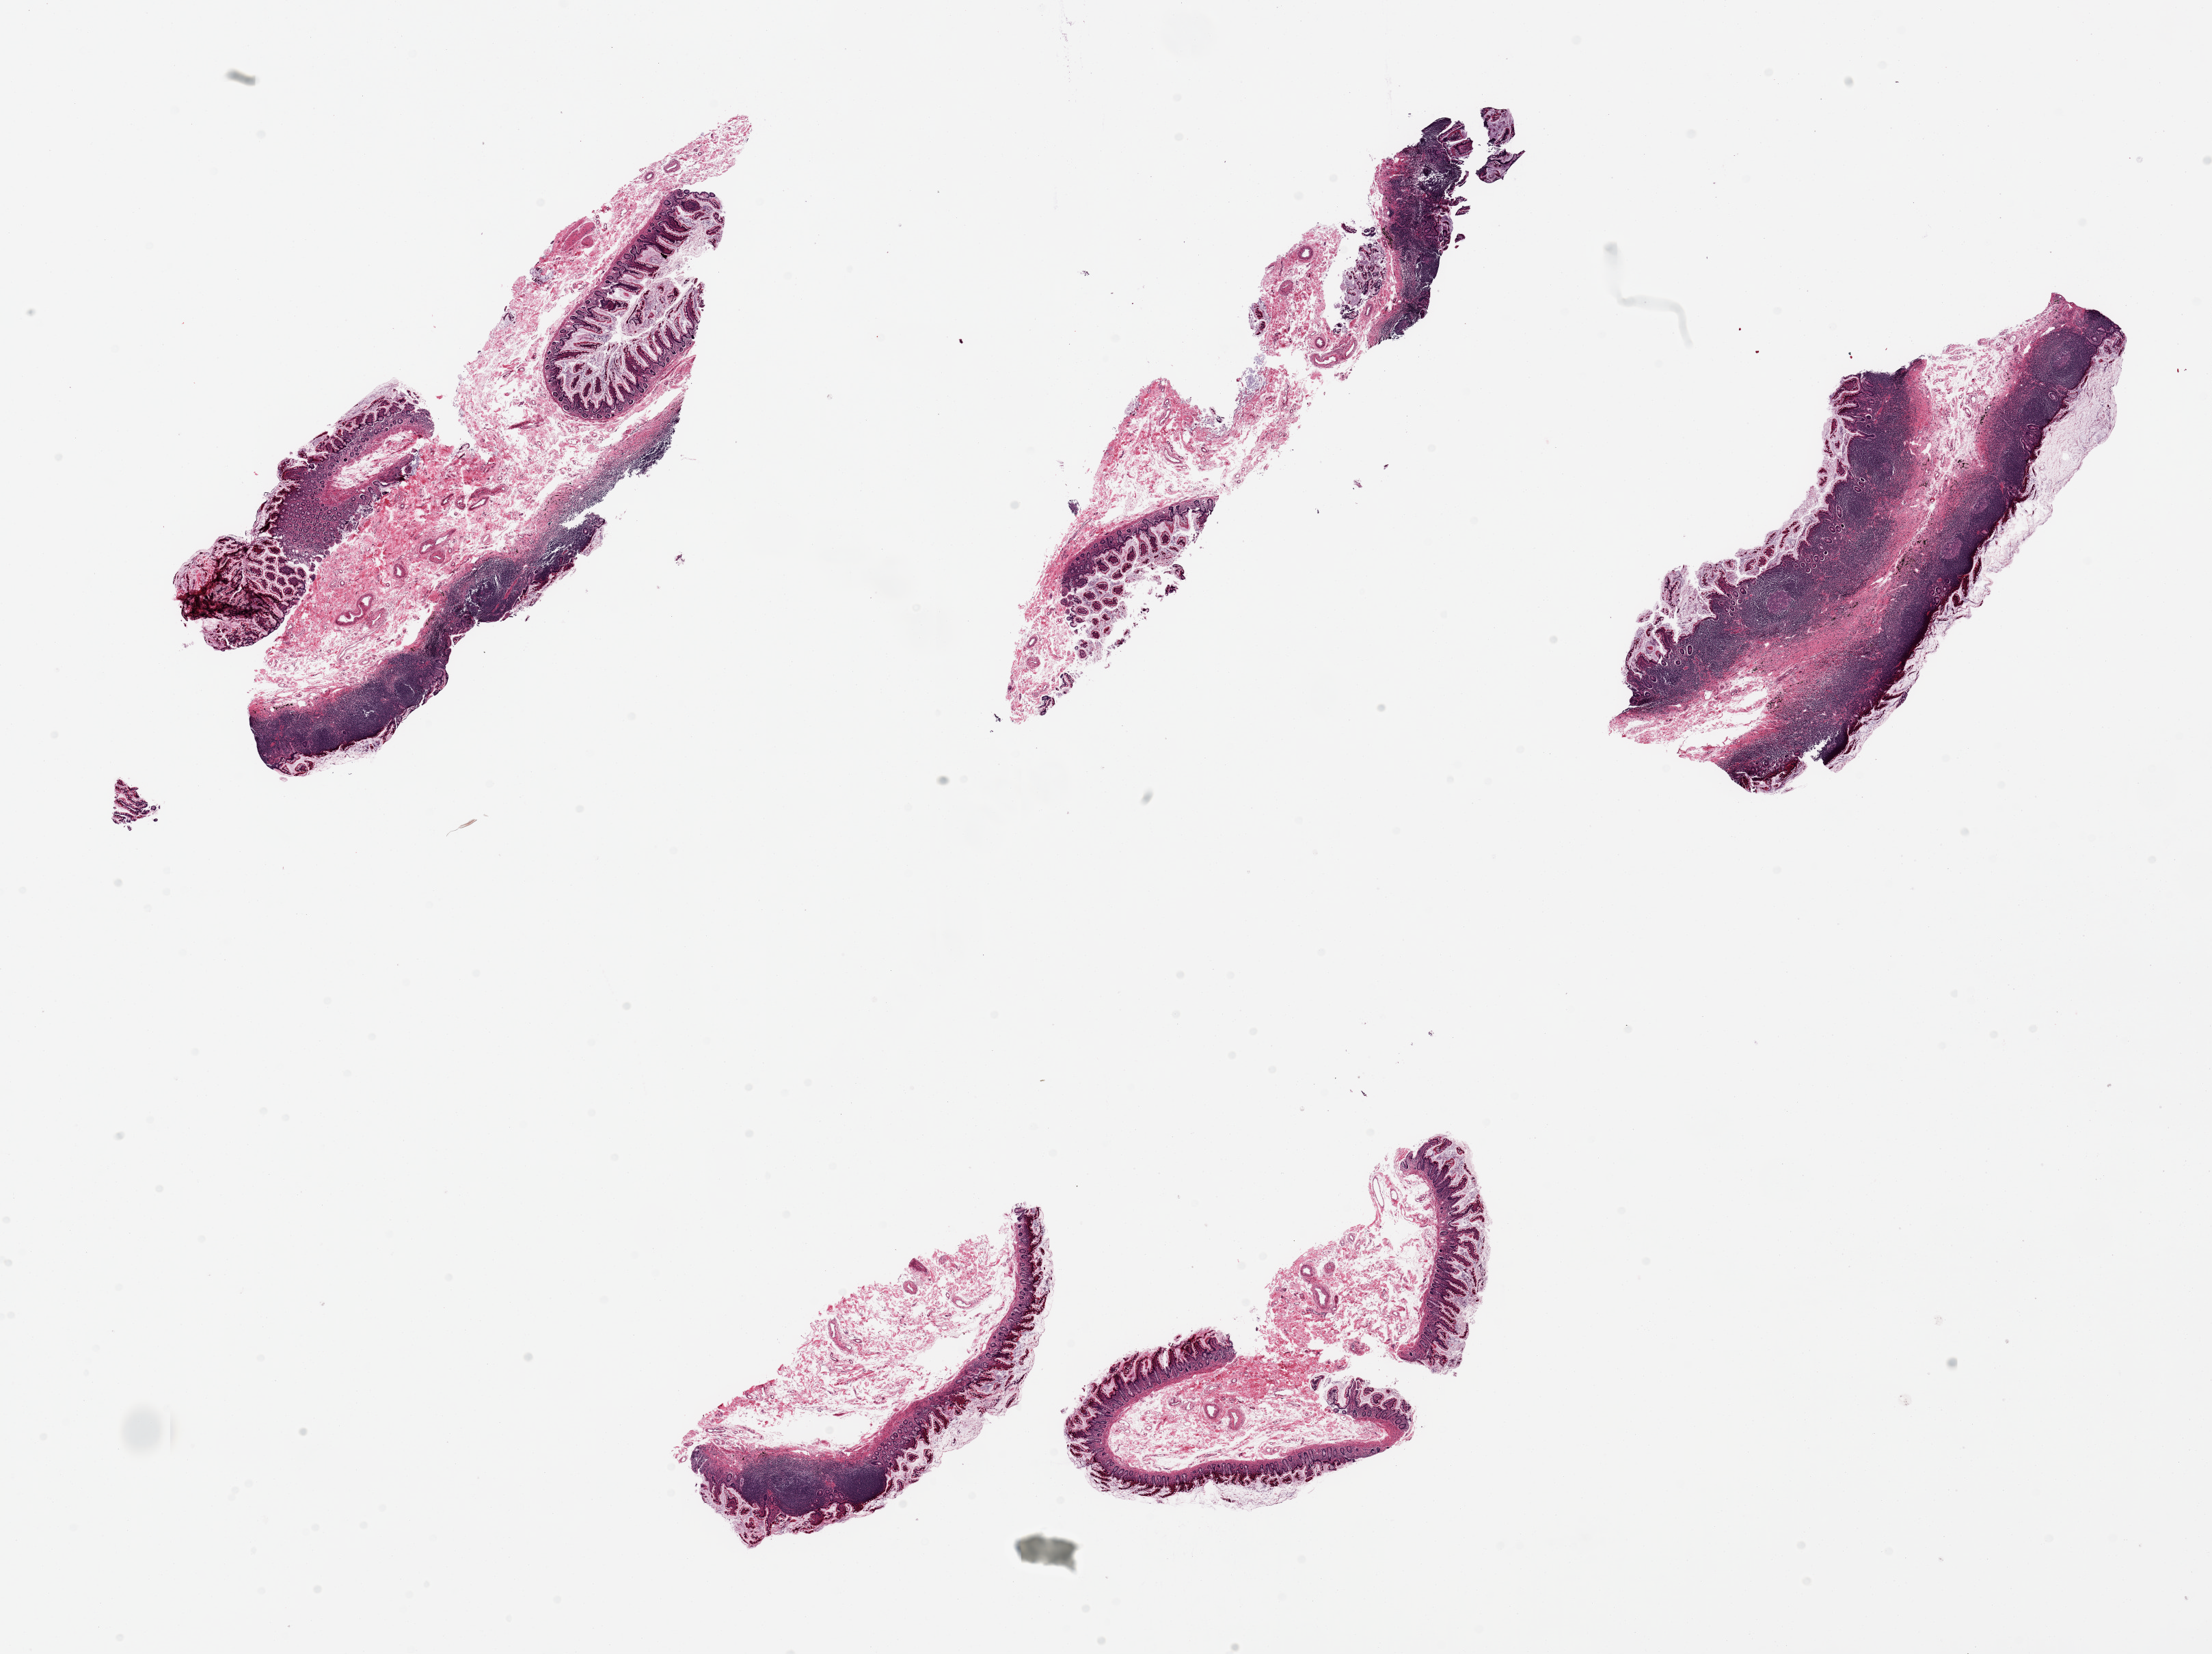
Whole-slide image, H&E stain, a low-resolution overview of the entire scanned area, about 25.6 x 19.1 mm (from a 20x scan). PAXgene-fixed, paraffin-embedded tissue. Section of ileum (target tissue). Tissue donor sample. Donor: female.
Review note (as recorded): 5 pieces, 4 with plentiful lymphoid tissue; well dissected without muscle.